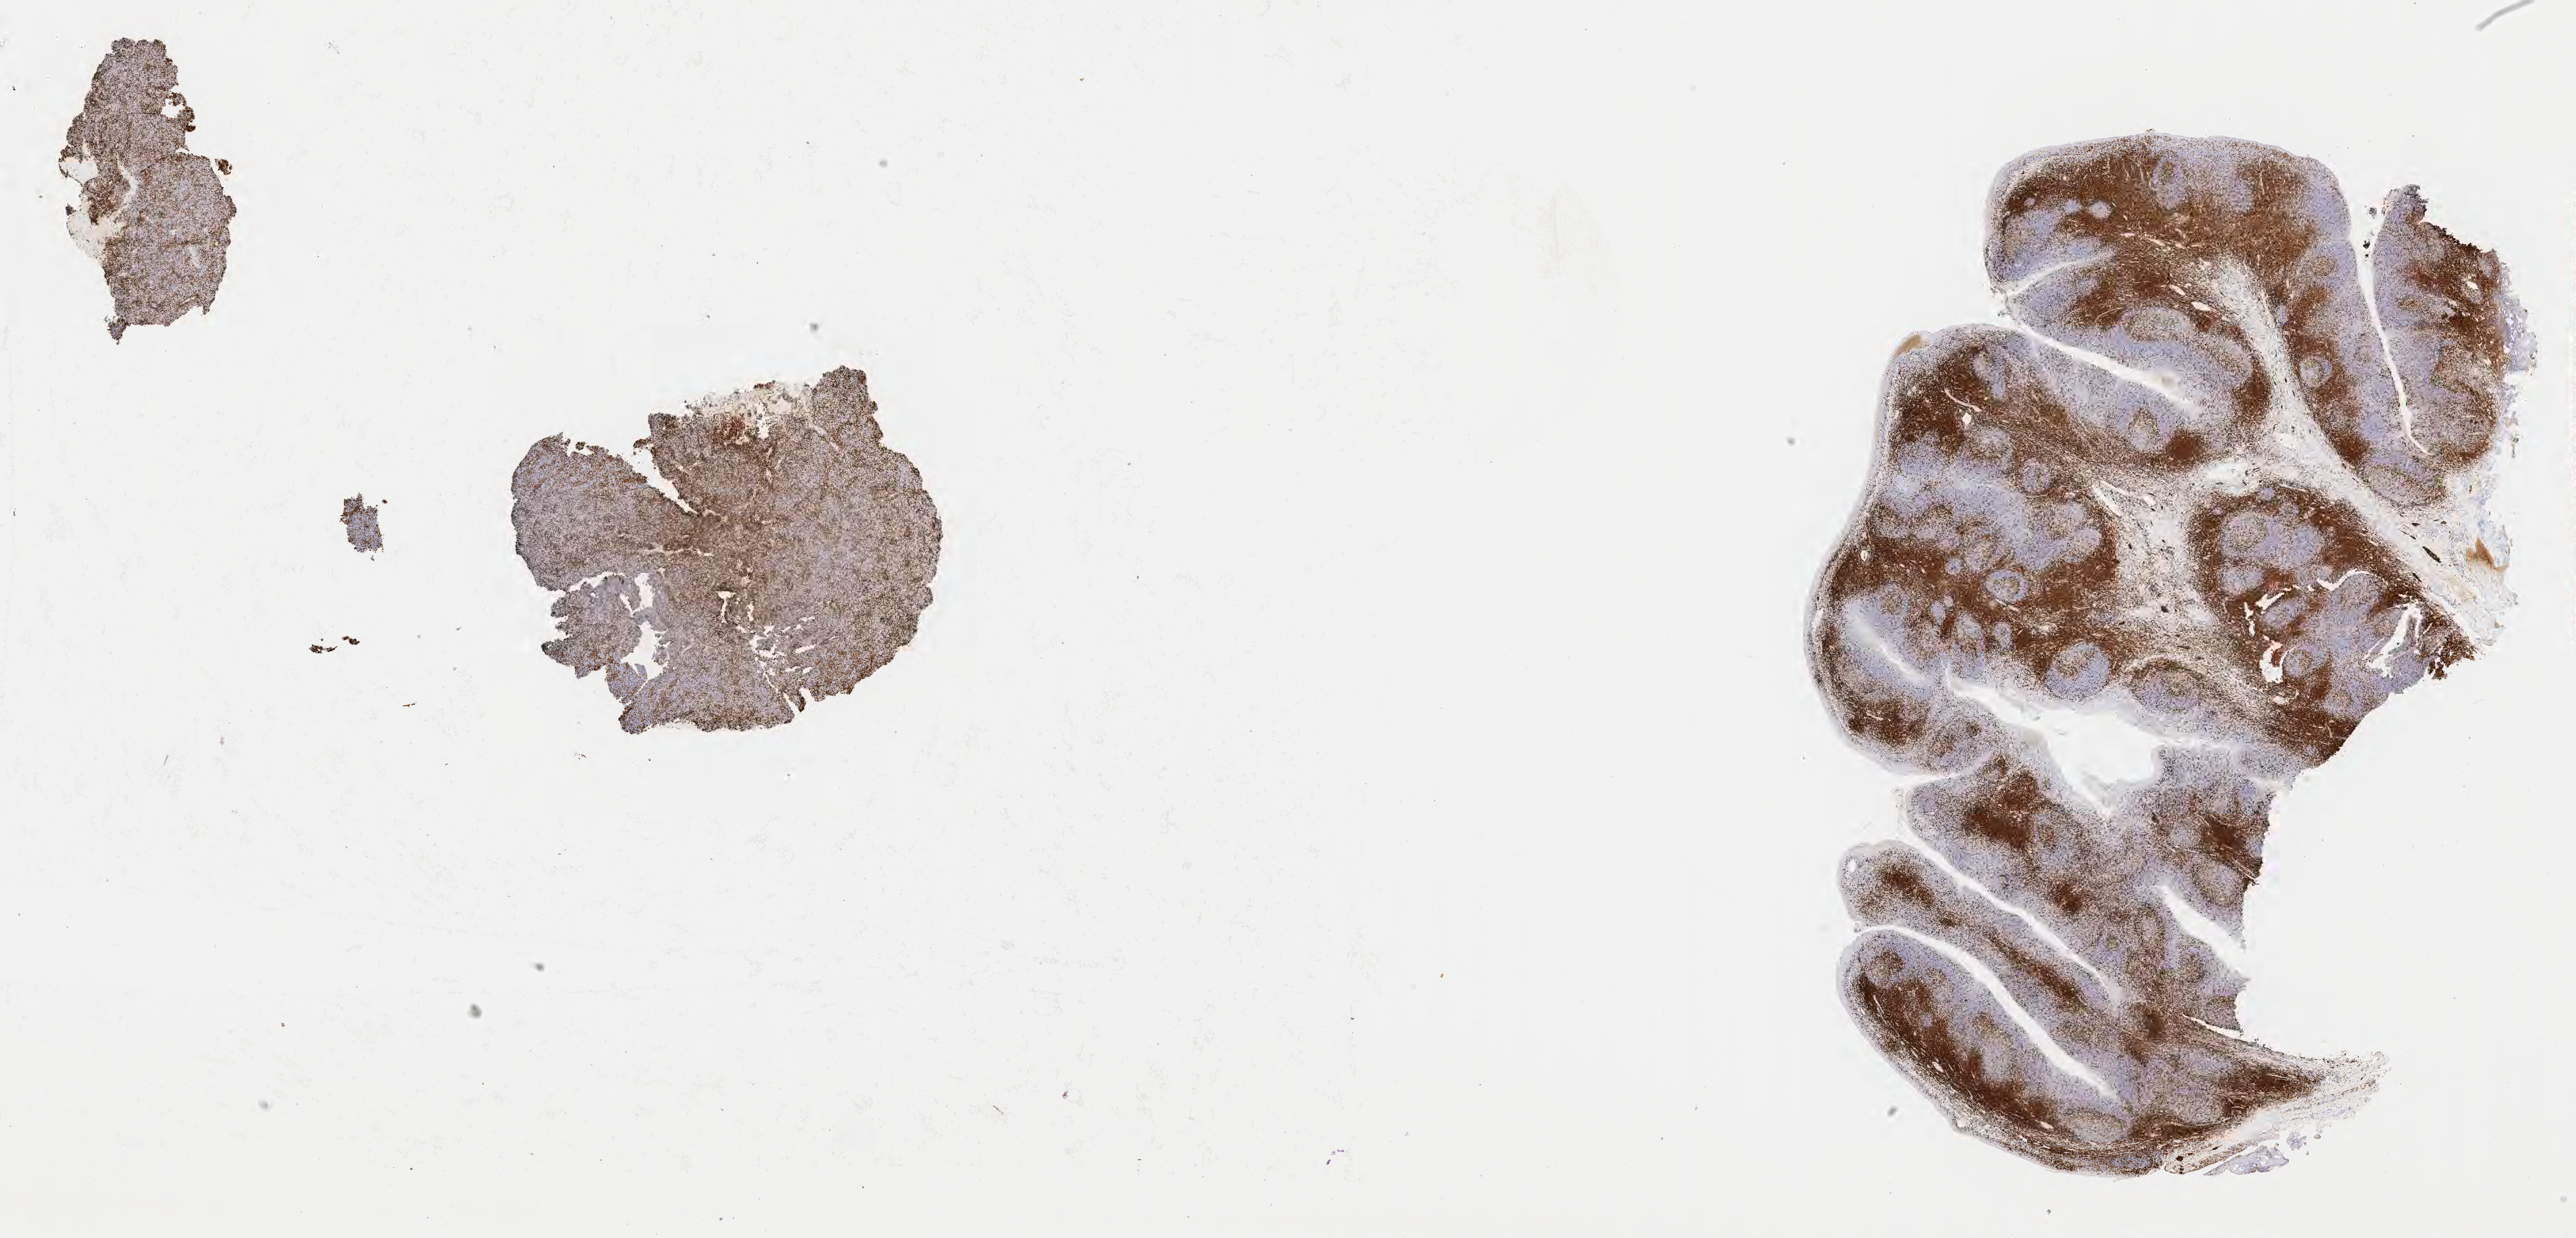
Immunohistochemistry (IHC) whole-slide image stained for CD3, low-resolution overview of the scanned area, about 30.7 x 14.8 mm, specimen: tumor tissue, anatomic site: lymph node. Patient female; 51 years old.
* histologic diagnosis: Diffuse large B-cell lymphoma, NOS